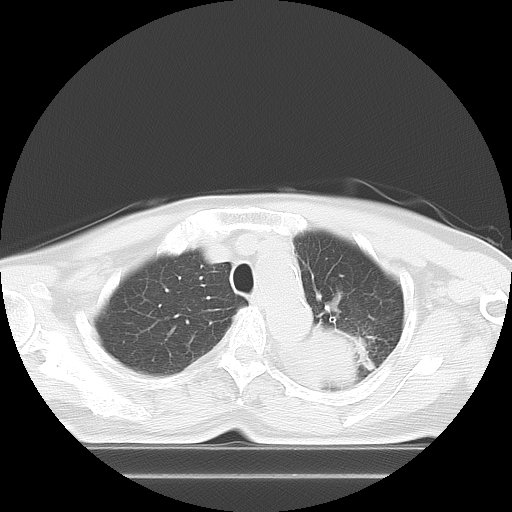
Chest CT, one axial slice. Slice 10 of 21 in the series (ordered by position). Lung window (W 1500 / L -600 HU). 512 × 512 image matrix, field of view 350 × 350 mm. Patient: female, 74 years. From the clinical record (not read from this slice): clinical TNM (as recorded): T3 N1 M1c.
Structures marked on this image (bounding box drawn by a radiologist):
- lung tumour (recorded histology: small cell carcinoma): bounding box <301,315,360,395> (left, top, right, bottom; pixels)